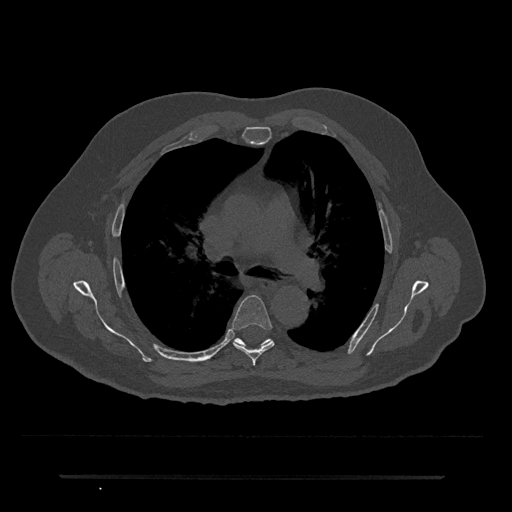
CT including the spine, one axial slice. Position 471 of 797 along the scan axis. Bone window (W 1800 / L 400 HU). 0.5 mm slice thickness. 512 × 512 image matrix. Male patient, age 69 years. Case-level facts recorded for this patient, not image findings: primary cancer: prostate.
Annotated regions visible in this slice (semi-automatic segmentation, software-assisted and operator-edited):
- T5 vertebra: bounding box [x1, y1, x2, y2] px = [231, 295, 274, 365]
- T6 vertebra: [235, 338, 242, 345]